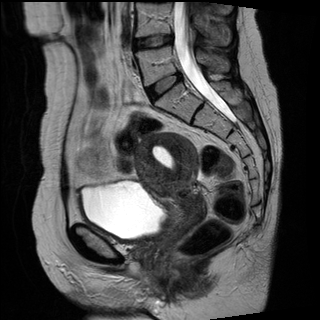
Pelvic MRI for cervical cancer, one sagittal slice; slice 14 of 27 in the series (ordered by position); T2-weighted; 1.5 T; TE 89 ms, TR 2740 ms; 320 × 320 image matrix. Female patient, age 42 years.
Outlined on this slice (outlined manually by an expert reader):
- uterus and cervix: bounding box [x1, y1, x2, y2] px = [133, 131, 208, 246]